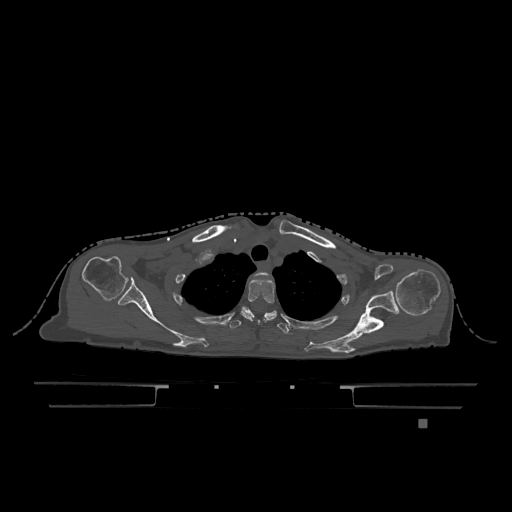
CT including the spine, one axial slice; slice 952 of 1317 in the series (ordered by position); bone window (W 1800 / L 400 HU); 0.5 mm slice thickness; 512 × 512 image matrix. Female patient, age 74 years. From the clinical record (not read from this slice): primary cancer: lung; vertebrae with lytic lesions (as recorded): T1, T4, T5, T6, L4, L5.
Structures marked on this image (semi-automatic segmentation, software-assisted and operator-edited):
- T1 vertebra: bounding box <257,273,268,275> (left, top, right, bottom; pixels)
- T2 vertebra: <241,278,277,321>
- T3 vertebra: <229,308,289,334>
- T6 vertebra: <242,307,277,317>